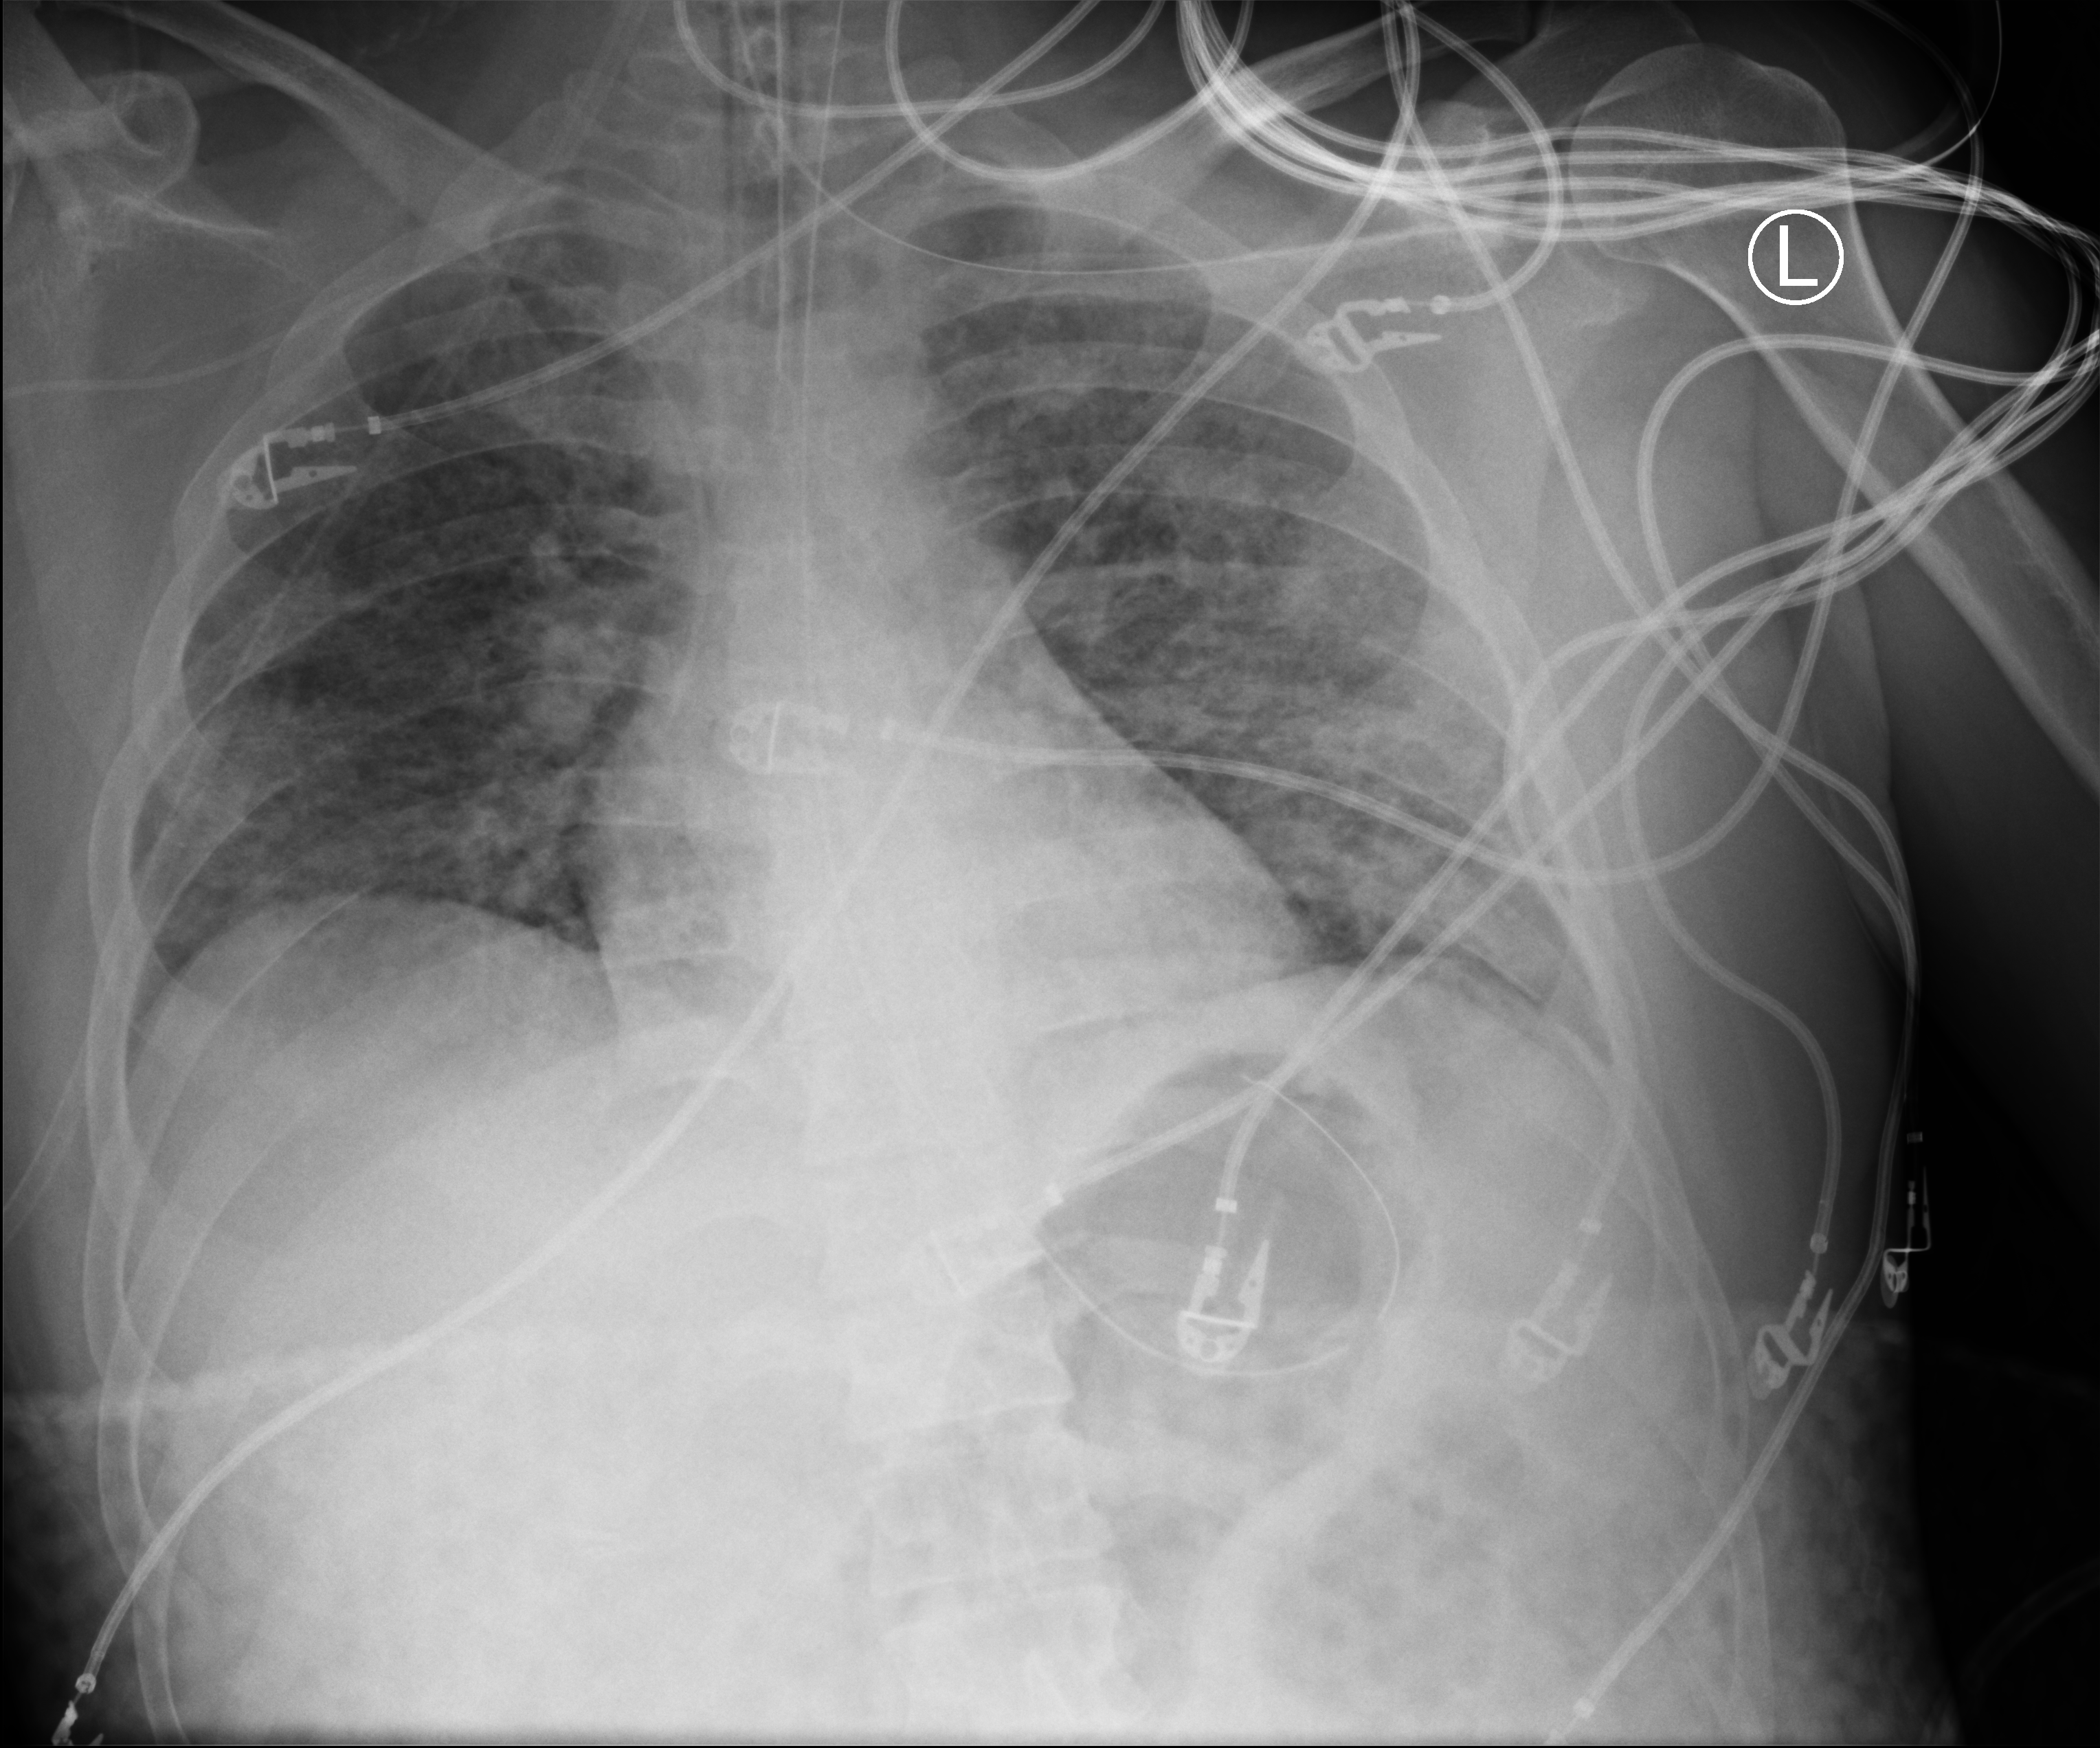
Chest X-ray (portable). Male patient hospitalised with COVID-19, age 18–59 years.
Admission-level facts for this patient (not findings on this image; timing relative to this image not recorded):
- COPD (admission record): no
- other chronic lung disease (admission record): no